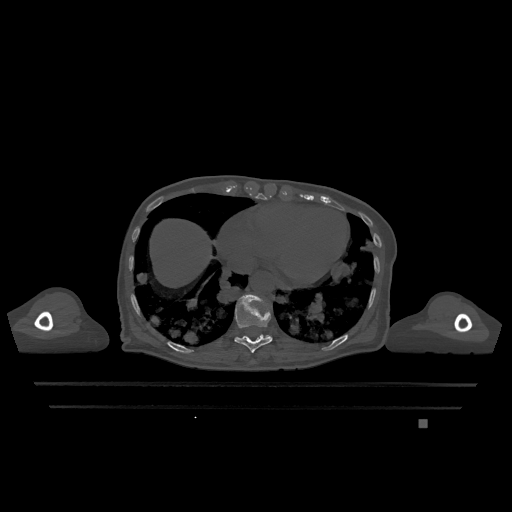
CT including the spine, one axial slice. Bone window (W 1800 / L 400 HU). 512 × 512 image matrix, field of view 500 × 500 mm. Patient: female, 74 years. From the clinical record (not read from this slice): primary cancer: lung; vertebrae with lytic lesions (as recorded): T1, T4, T5, T6, L4, L5.
Annotated regions visible in this slice (semi-automatically segmented with operator editing):
- T10 vertebra: bounding box <234,294,273,353> (left, top, right, bottom; pixels)